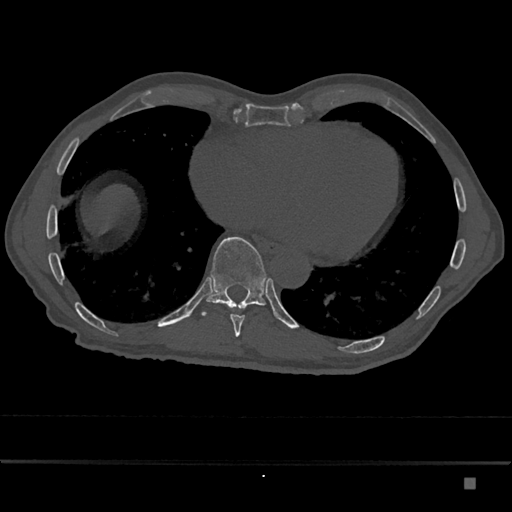
CT including the spine, one axial slice. Slice 768 of 797 in the series (ordered by position). 120 kVp. Bone window (W 1800 / L 400 HU). 0.5 mm slice thickness. 512 × 512 image matrix. Patient: male, 72 years. From the clinical record (not read from this slice): primary cancer: prostate.
Annotated regions visible in this slice (semi-automatic segmentation, software-assisted and operator-edited):
- T10 vertebra: box from (x=201, y=237) to (x=267, y=316) px
- T9 vertebra: (x=231, y=306)–(x=245, y=337)